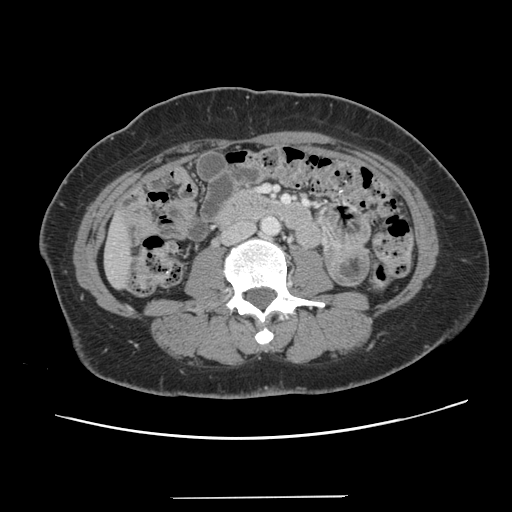
Contrast-enhanced abdominal CT, one axial slice. Position 23 of 141 along the scan axis. 120 kVp. Intravenous contrast given. Soft-tissue window (W 400 / L 40 HU). 512 × 512 image matrix. Female patient, age 53 years. From the clinical record (not read from this slice): diagnosis: colorectal cancer liver metastases, imaged before liver resection.
Outlined on this slice (outlined manually by an expert reader):
- liver: bounding box (x1, y1, x2, y2) in pixels: (105, 218, 132, 288)
- planned liver remnant (the part of the liver to remain after resection): (106, 218, 132, 287)